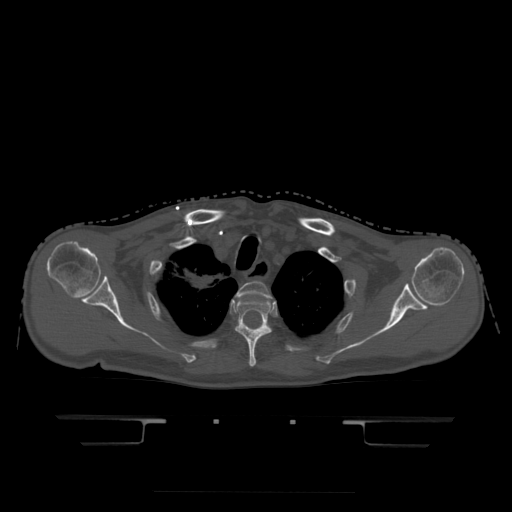
CT including the spine, one axial slice; position 372 of 522 along the scan axis; bone window (W 1800 / L 400 HU); 1.25 mm slice thickness; 512 × 512 image matrix, field of view 436 × 436 mm. Patient age 68 years. From the clinical record (not read from this slice): primary cancer: urothelial.
Annotated regions visible in this slice (semi-automatically segmented with operator editing):
- T2 vertebra: bounding box [x1, y1, x2, y2] px = [237, 282, 271, 299]
- T3 vertebra: [236, 299, 273, 367]